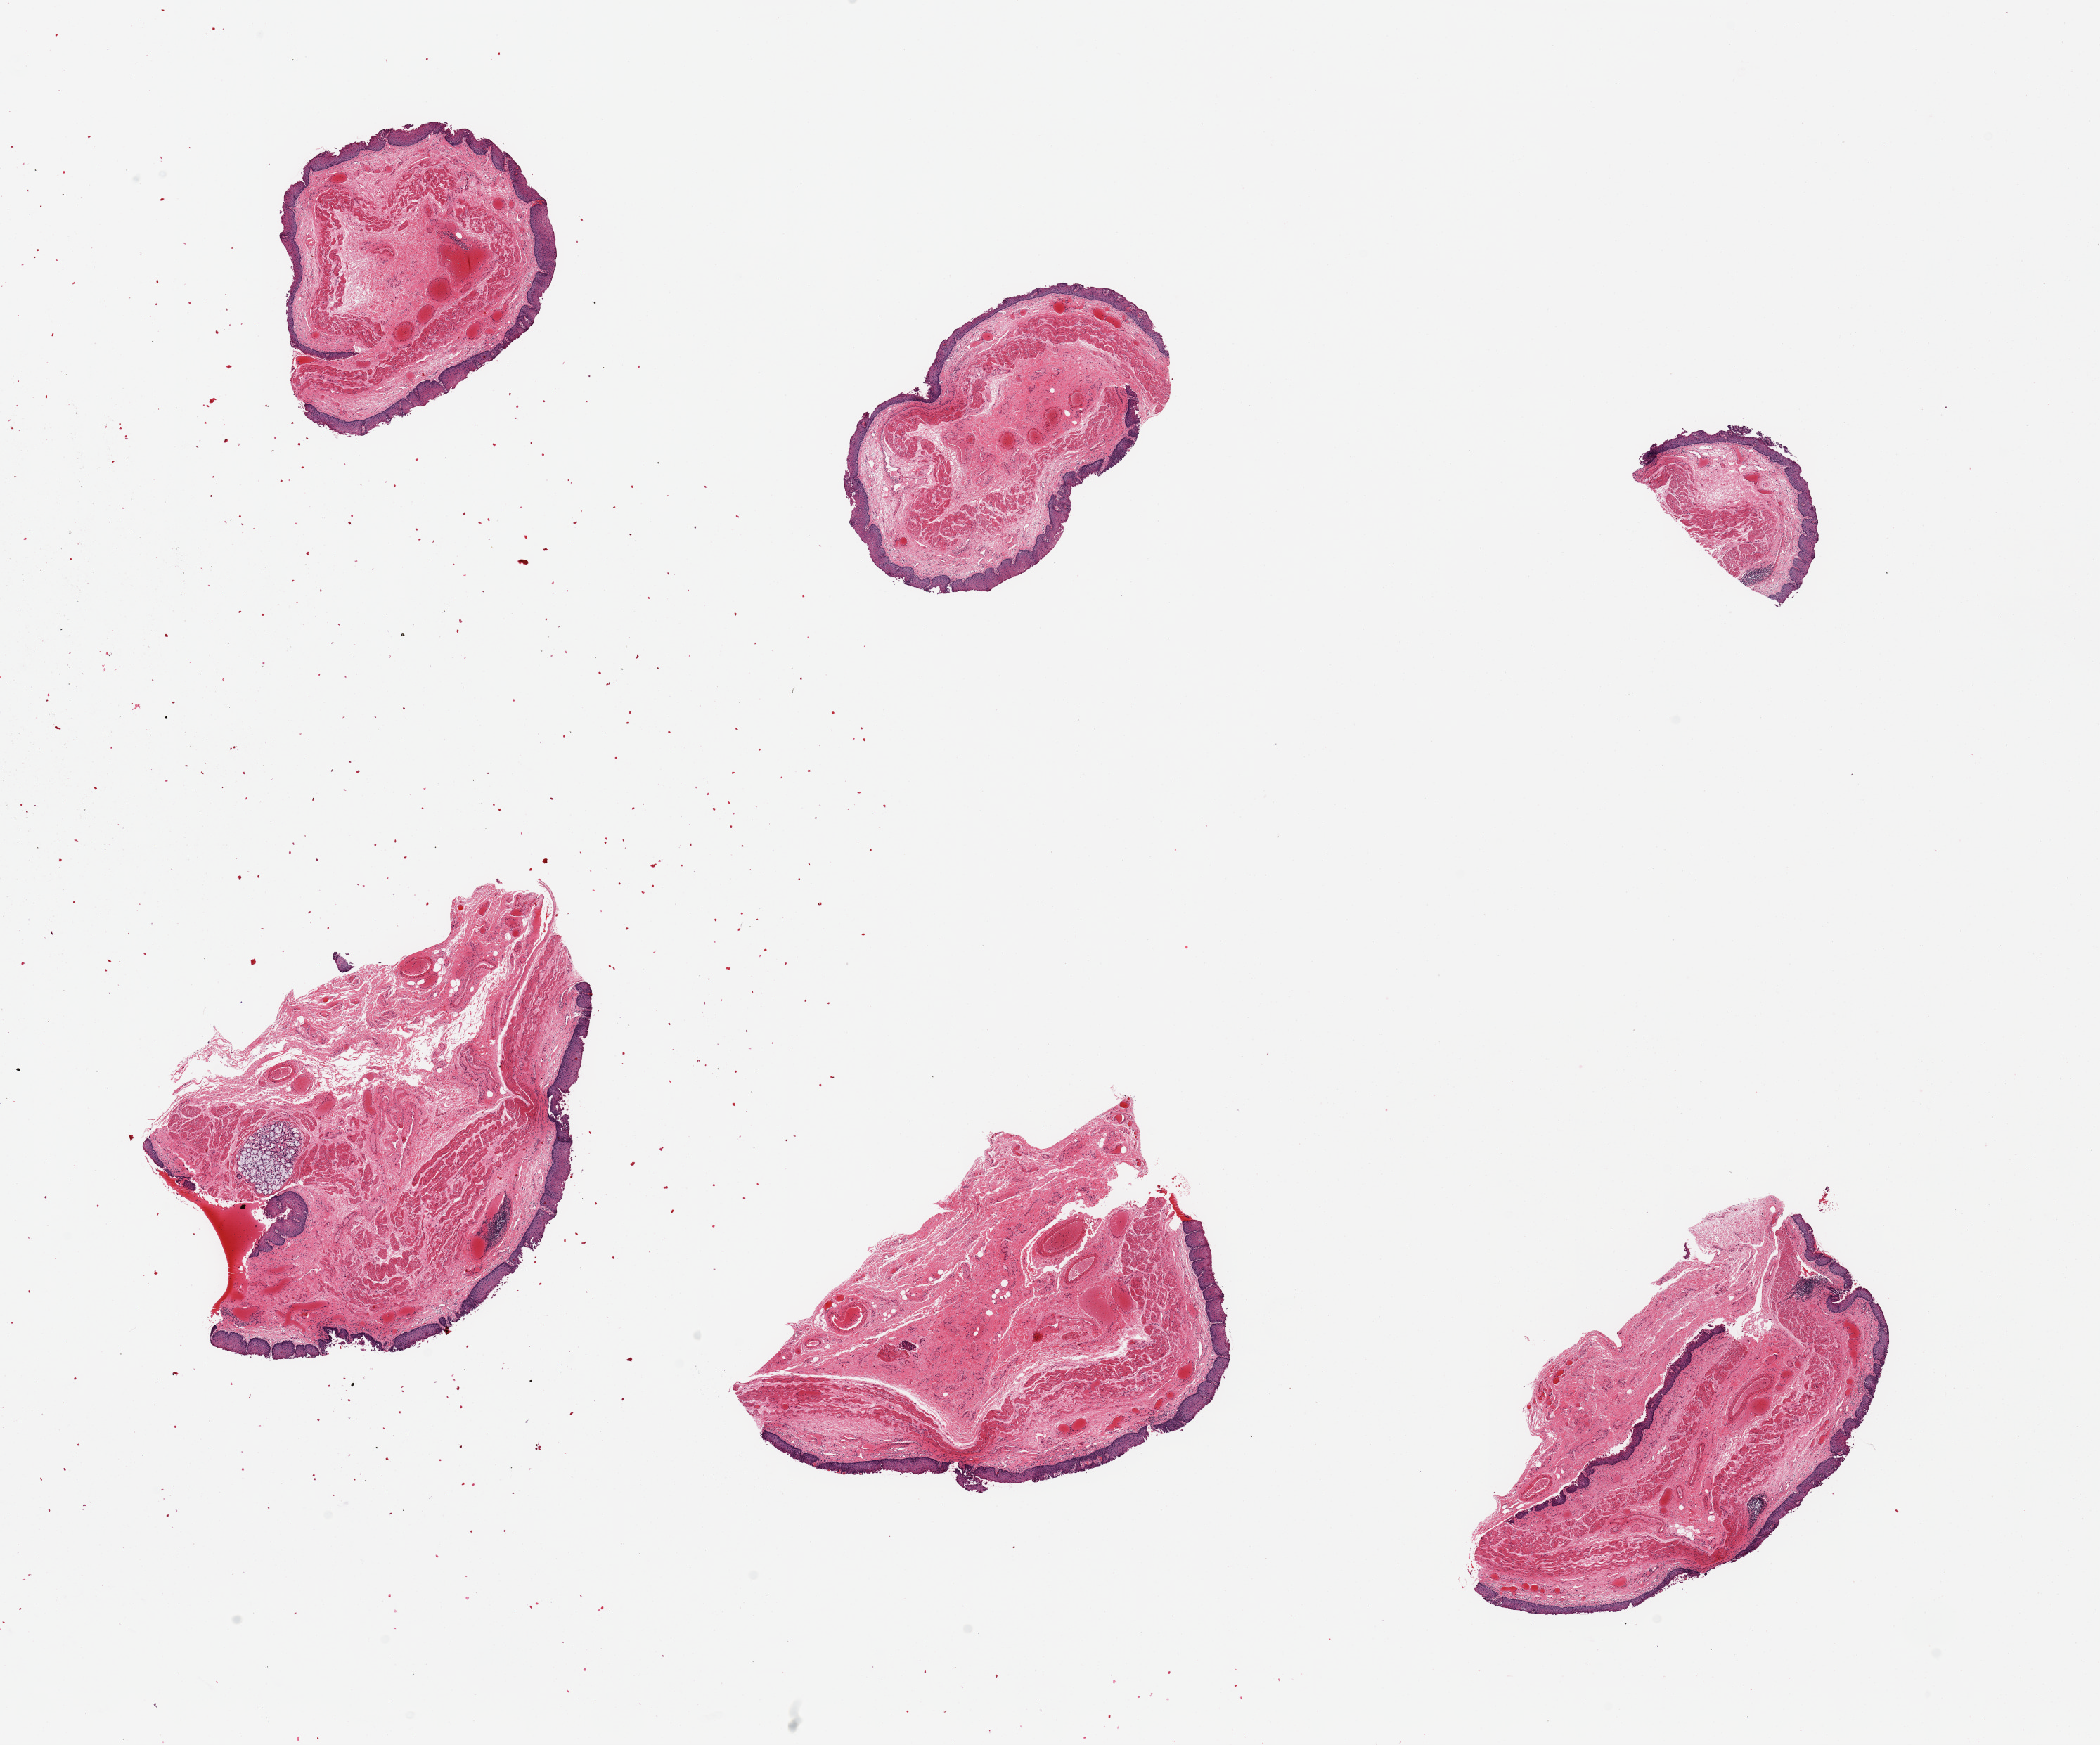
Whole-slide image, H&E stain, brightfield, low-resolution overview of the scanned area, about 23.6 x 19.6 mm (acquisition: 20x scan). PAXgene-fixed paraffin-embedded (PFPE) section. Section of esophageal mucous membrane (target tissue). Donor tissue sample. Male donor.
Review note (as recorded): 6 pieces; superficial epithelial sloughing; well dissected.